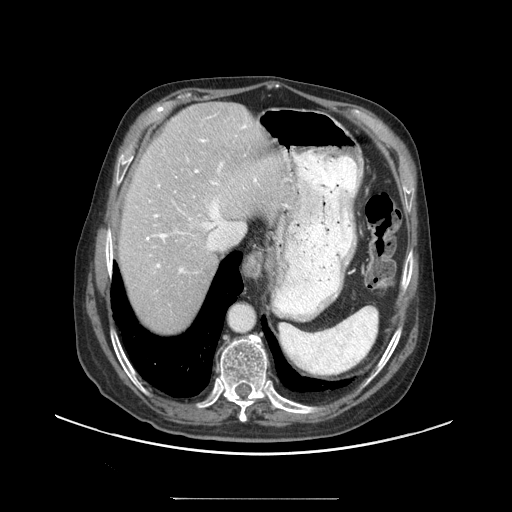
Contrast-enhanced abdominal CT (liver protocol), one axial slice. Slice 78 of 97 in the series (ordered by position). 140 kVp. Soft-tissue window (W 400 / L 40 HU). 2.5 mm slice thickness. 512 × 512 image matrix, field of view 450 × 450 mm. From the clinical record (not read from this slice): diagnosis: hepatocellular carcinoma (patient treated with transarterial chemoembolisation; whether this scan precedes or follows treatment is not stated here); TNM stage (as recorded): Stage-IIIC; Child-Pugh class: A.
Annotated regions visible in this slice (semi-automatic segmentation, software-assisted and operator-edited):
- abdominal aorta: bounding box <230,303,256,331> (left, top, right, bottom; pixels)
- liver parenchyma outside the tumour (the mass and vessels are separate outlines, so this box may not span the whole liver): <118,102,295,332>
- liver vessels: <146,124,287,273>